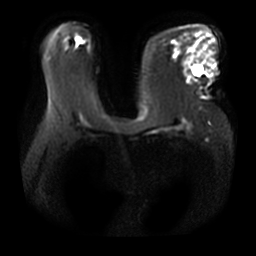
Breast MRI, one axial slice. Slice 21 of 36 in the series (ordered by position). Diffusion-weighted series; image 2 of 4 stored at this slice position (different b-values; order by instance number). 3 T. 5 mm slice thickness. 256 × 256 image matrix, field of view 380 × 380 mm. Female patient.
Outlined on this slice (outlined manually by an expert reader):
- tumour on diffusion-weighted imaging: bounding box <192,67,201,76> (left, top, right, bottom; pixels)